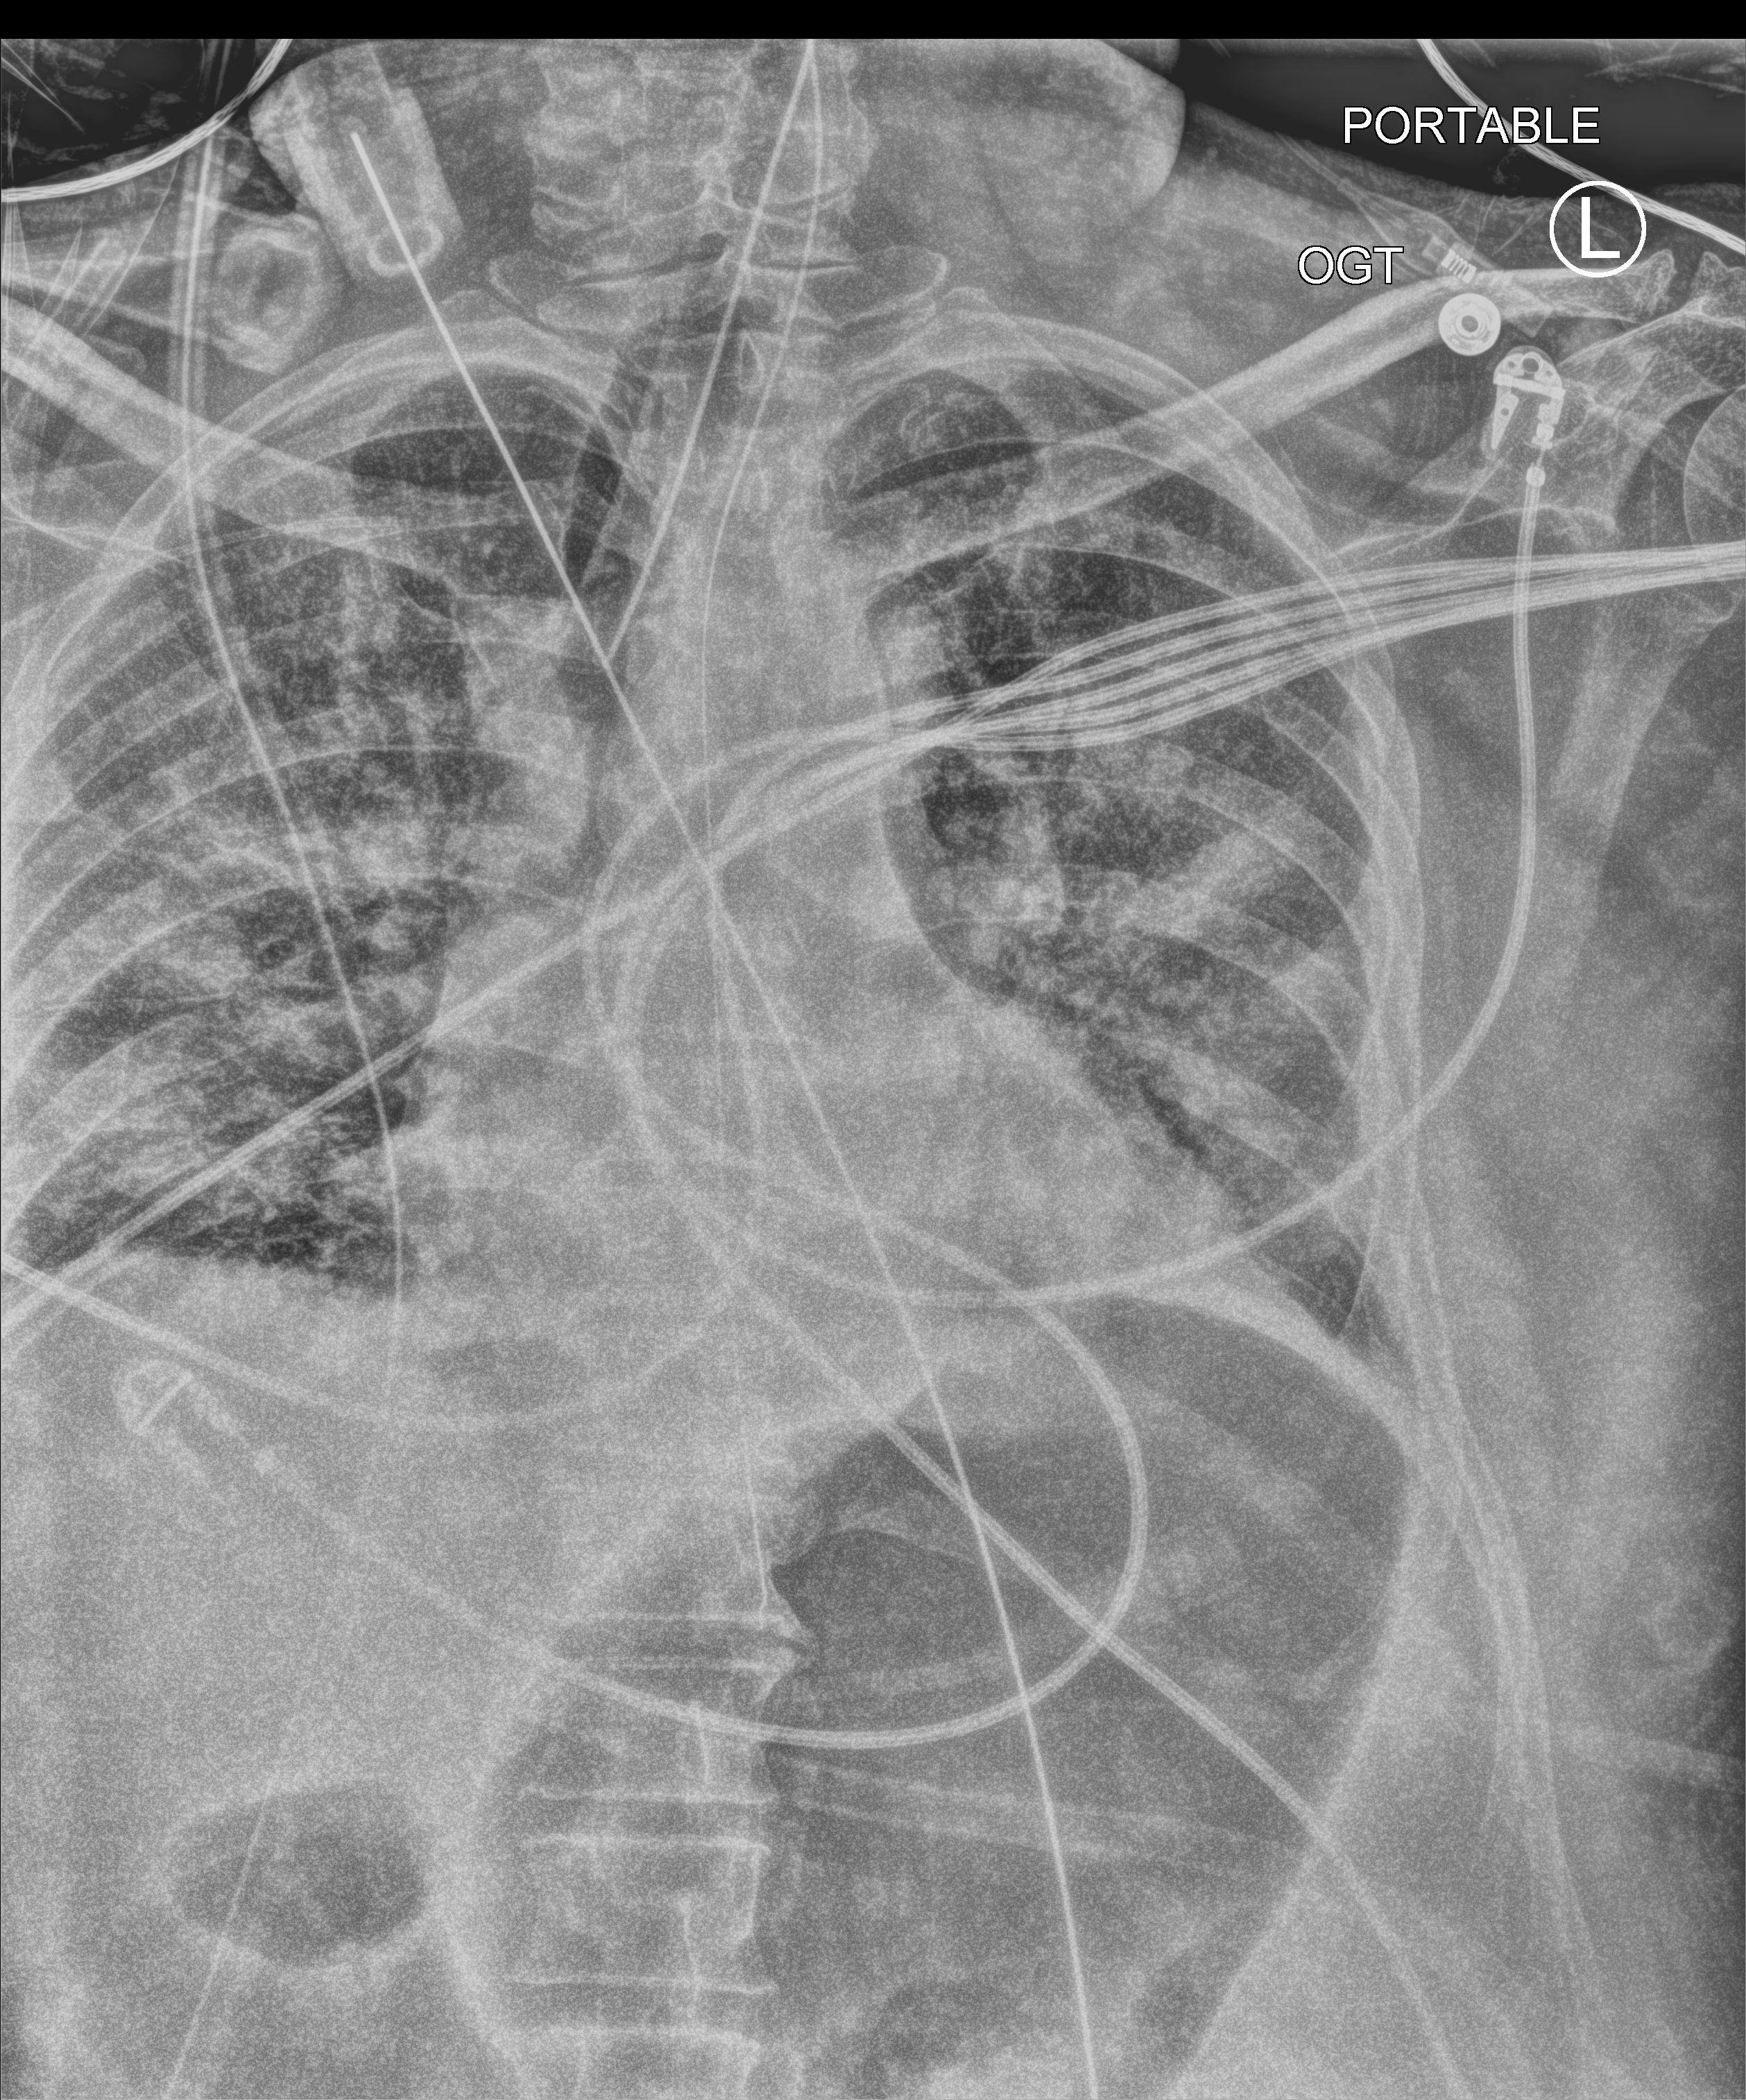
Chest X-ray (portable); anteroposterior (AP) projection. Patient hospitalised with COVID-19; male, aged 60–74 years.
Admission-level facts for this patient (not findings on this image; timing relative to this image not recorded): chronic kidney disease (admission record): no; admitted to intensive care during this hospital stay: yes.